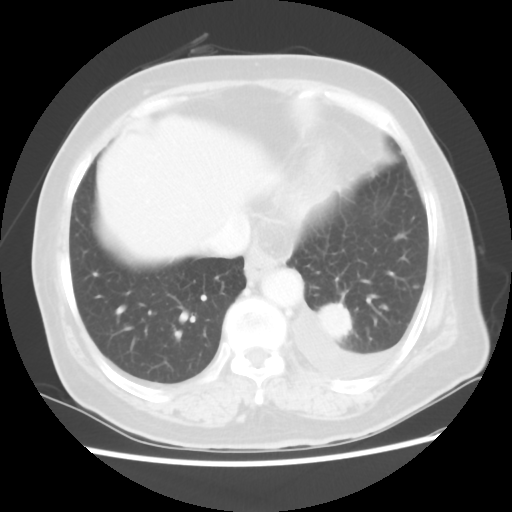
Chest CT, one axial slice. Slice 12 of 80 in the series (ordered by position). Lung window (W 1500 / L -600 HU). 5 mm slice thickness. 512 × 512 image matrix, field of view 343 × 343 mm. Patient: female, 68 years. Case-level facts recorded for this patient, not image findings: clinical TNM (as recorded): T1c N0 M1.
Structures marked on this image (bounding box drawn by a radiologist):
- lung tumour (recorded histology: adenocarcinoma): bounding box [x1, y1, x2, y2] px = [319, 299, 355, 343]